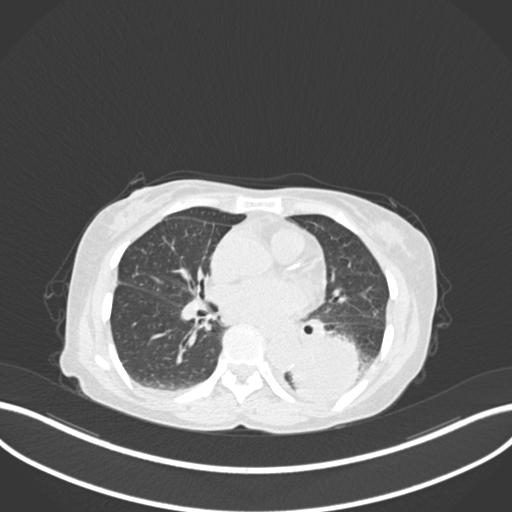
Chest CT, one axial slice; slice 70 of 233 in the series (ordered by position); reconstruction kernel B30f; 120 kVp; lung window (W 1500 / L -600 HU); 1 mm slice thickness; 512 × 512 image matrix, field of view 400 × 400 mm. Female patient, age 78 years. From the clinical record (not read from this slice): clinical TNM (as recorded): T3 N0 M1.
Structures marked on this image (rectangle marked by the reading radiologist):
- lung tumour (recorded histology: squamous cell carcinoma): box from (x=285, y=328) to (x=365, y=405) px